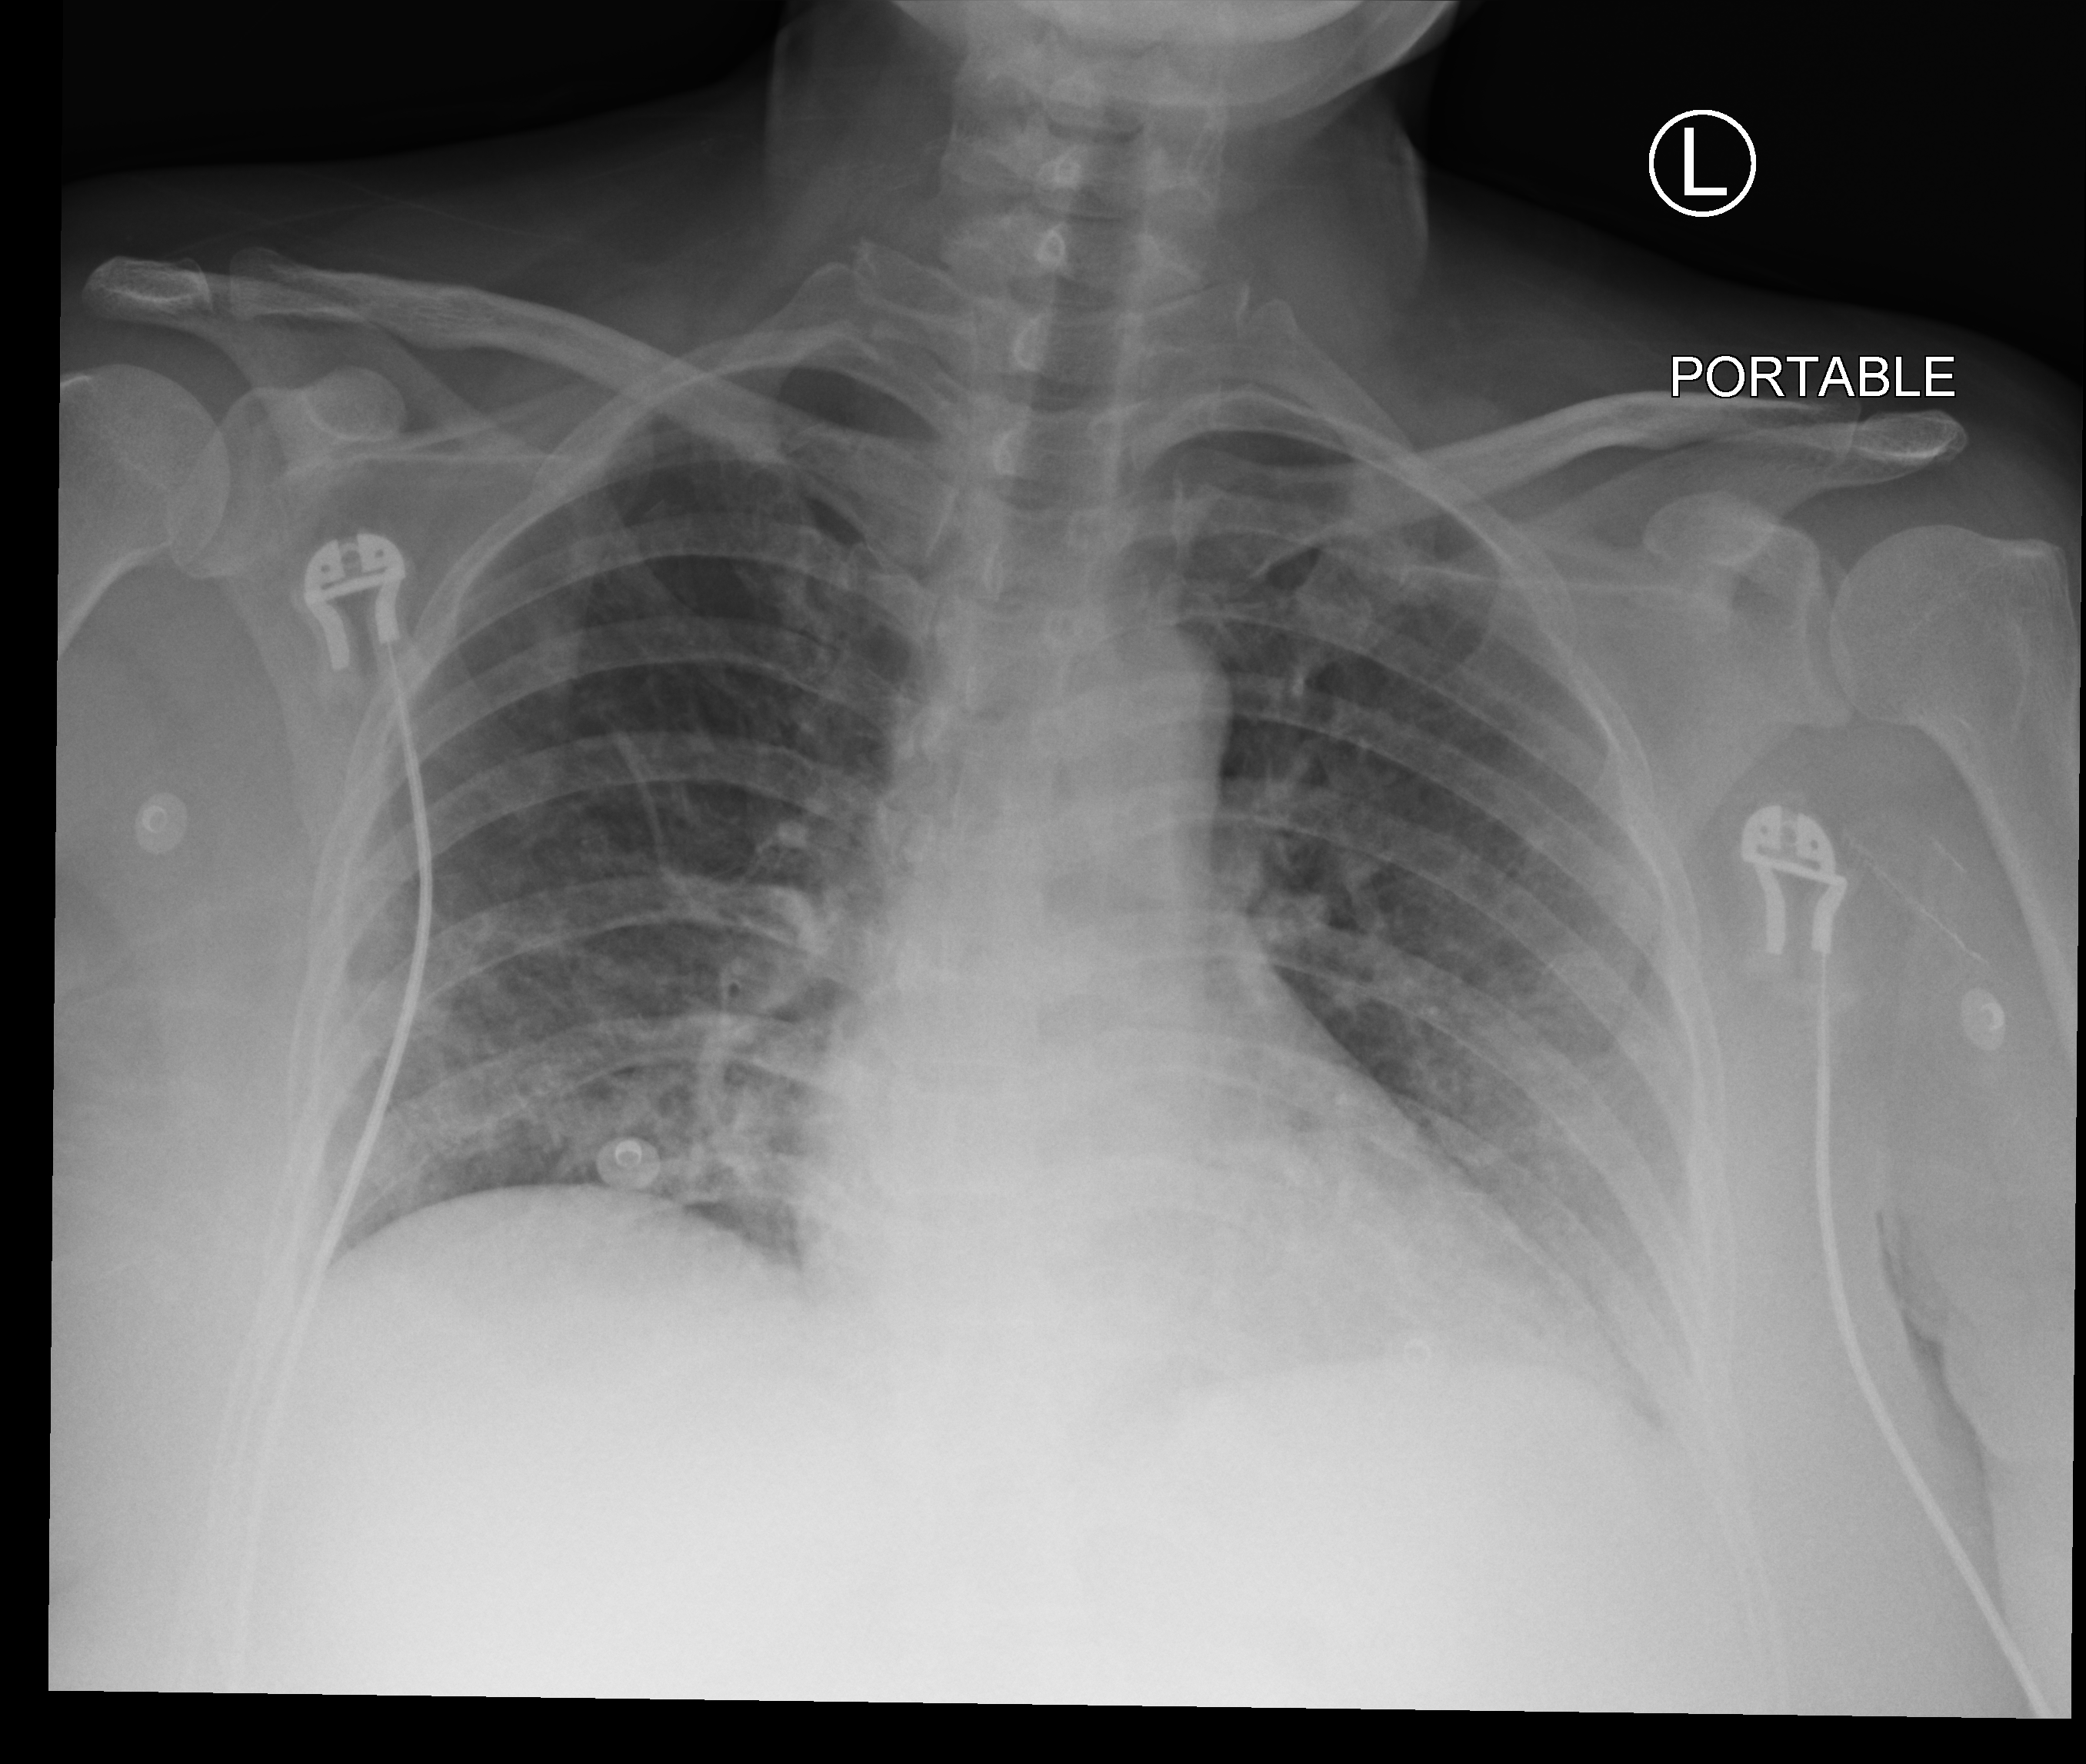
Portable chest radiograph. Patient hospitalised with COVID-19; female, aged 18–59 years.
Admission-level facts for this patient (not findings on this image; timing relative to this image not recorded):
- length of hospital stay: 5 days